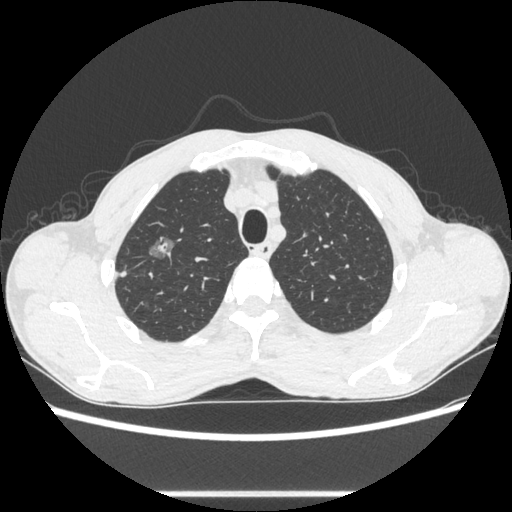
Chest CT, one axial slice; slice 488 of 600 in the series (ordered by position); 100 kVp; lung window (W 1500 / L -600 HU); 512 × 512 image matrix, field of view 357 × 357 mm. Patient: male, 54 years. Case-level facts recorded for this patient, not image findings: clinical TNM (as recorded): T1a N0 M0.
Outlined on this slice (rectangle marked by the reading radiologist):
- lung tumour (recorded histology: adenocarcinoma): box from (x=145, y=227) to (x=182, y=265) px